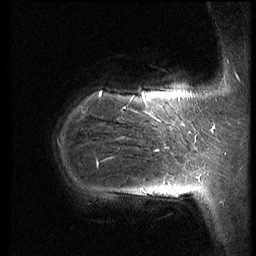
Breast MRI (dynamic contrast-enhanced), one sagittal slice; position 16 of 66 along the scan axis; dynamic contrast-enhanced series, image 2 of 3 at this slice position (ordered by acquisition); 1.5 T; TE 4.2 ms, TR 8.9 ms; 2.5 mm slice thickness; 256 × 256 image matrix, field of view 200 × 200 mm. Patient: female, 39 years. From the clinical record (not read from this slice): setting: breast cancer imaged before/during neoadjuvant chemotherapy; receptor status: HER2-positive.
Outlined on this slice (semi-automatically segmented with operator editing):
- analysis volume of interest (the breast-tissue region the enhancement analysis was run in; not a lesion): box from (x=52, y=75) to (x=188, y=218) px
- tumour enhancement mask (voxels above the 140 % enhancement threshold inside the analysis volume of interest): (x=97, y=92)–(x=165, y=167)